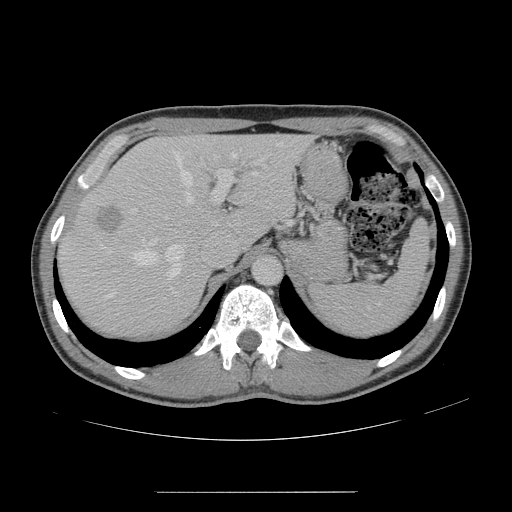
Contrast-enhanced abdominal CT, one axial slice. Position 110 of 178 along the scan axis. 120 kVp. Intravenous contrast given. Soft-tissue window (W 400 / L 40 HU). 512 × 512 image matrix. Male patient, age 53 years. Case-level facts recorded for this patient, not image findings: diagnosis: colorectal cancer liver metastases, imaged before liver resection; multiple liver metastases: yes; largest metastasis: 2.4 cm; chemotherapy before resection: yes.
Annotated regions visible in this slice (manually delineated by an expert):
- hepatic veins: bounding box (x1, y1, x2, y2) in pixels: (106, 142, 282, 298)
- liver: (59, 135, 307, 336)
- planned liver remnant (the part of the liver to remain after resection): (147, 136, 307, 244)
- portal vein (with intrahepatic branches): (131, 157, 266, 214)
- liver metastasis: (95, 207, 126, 236)